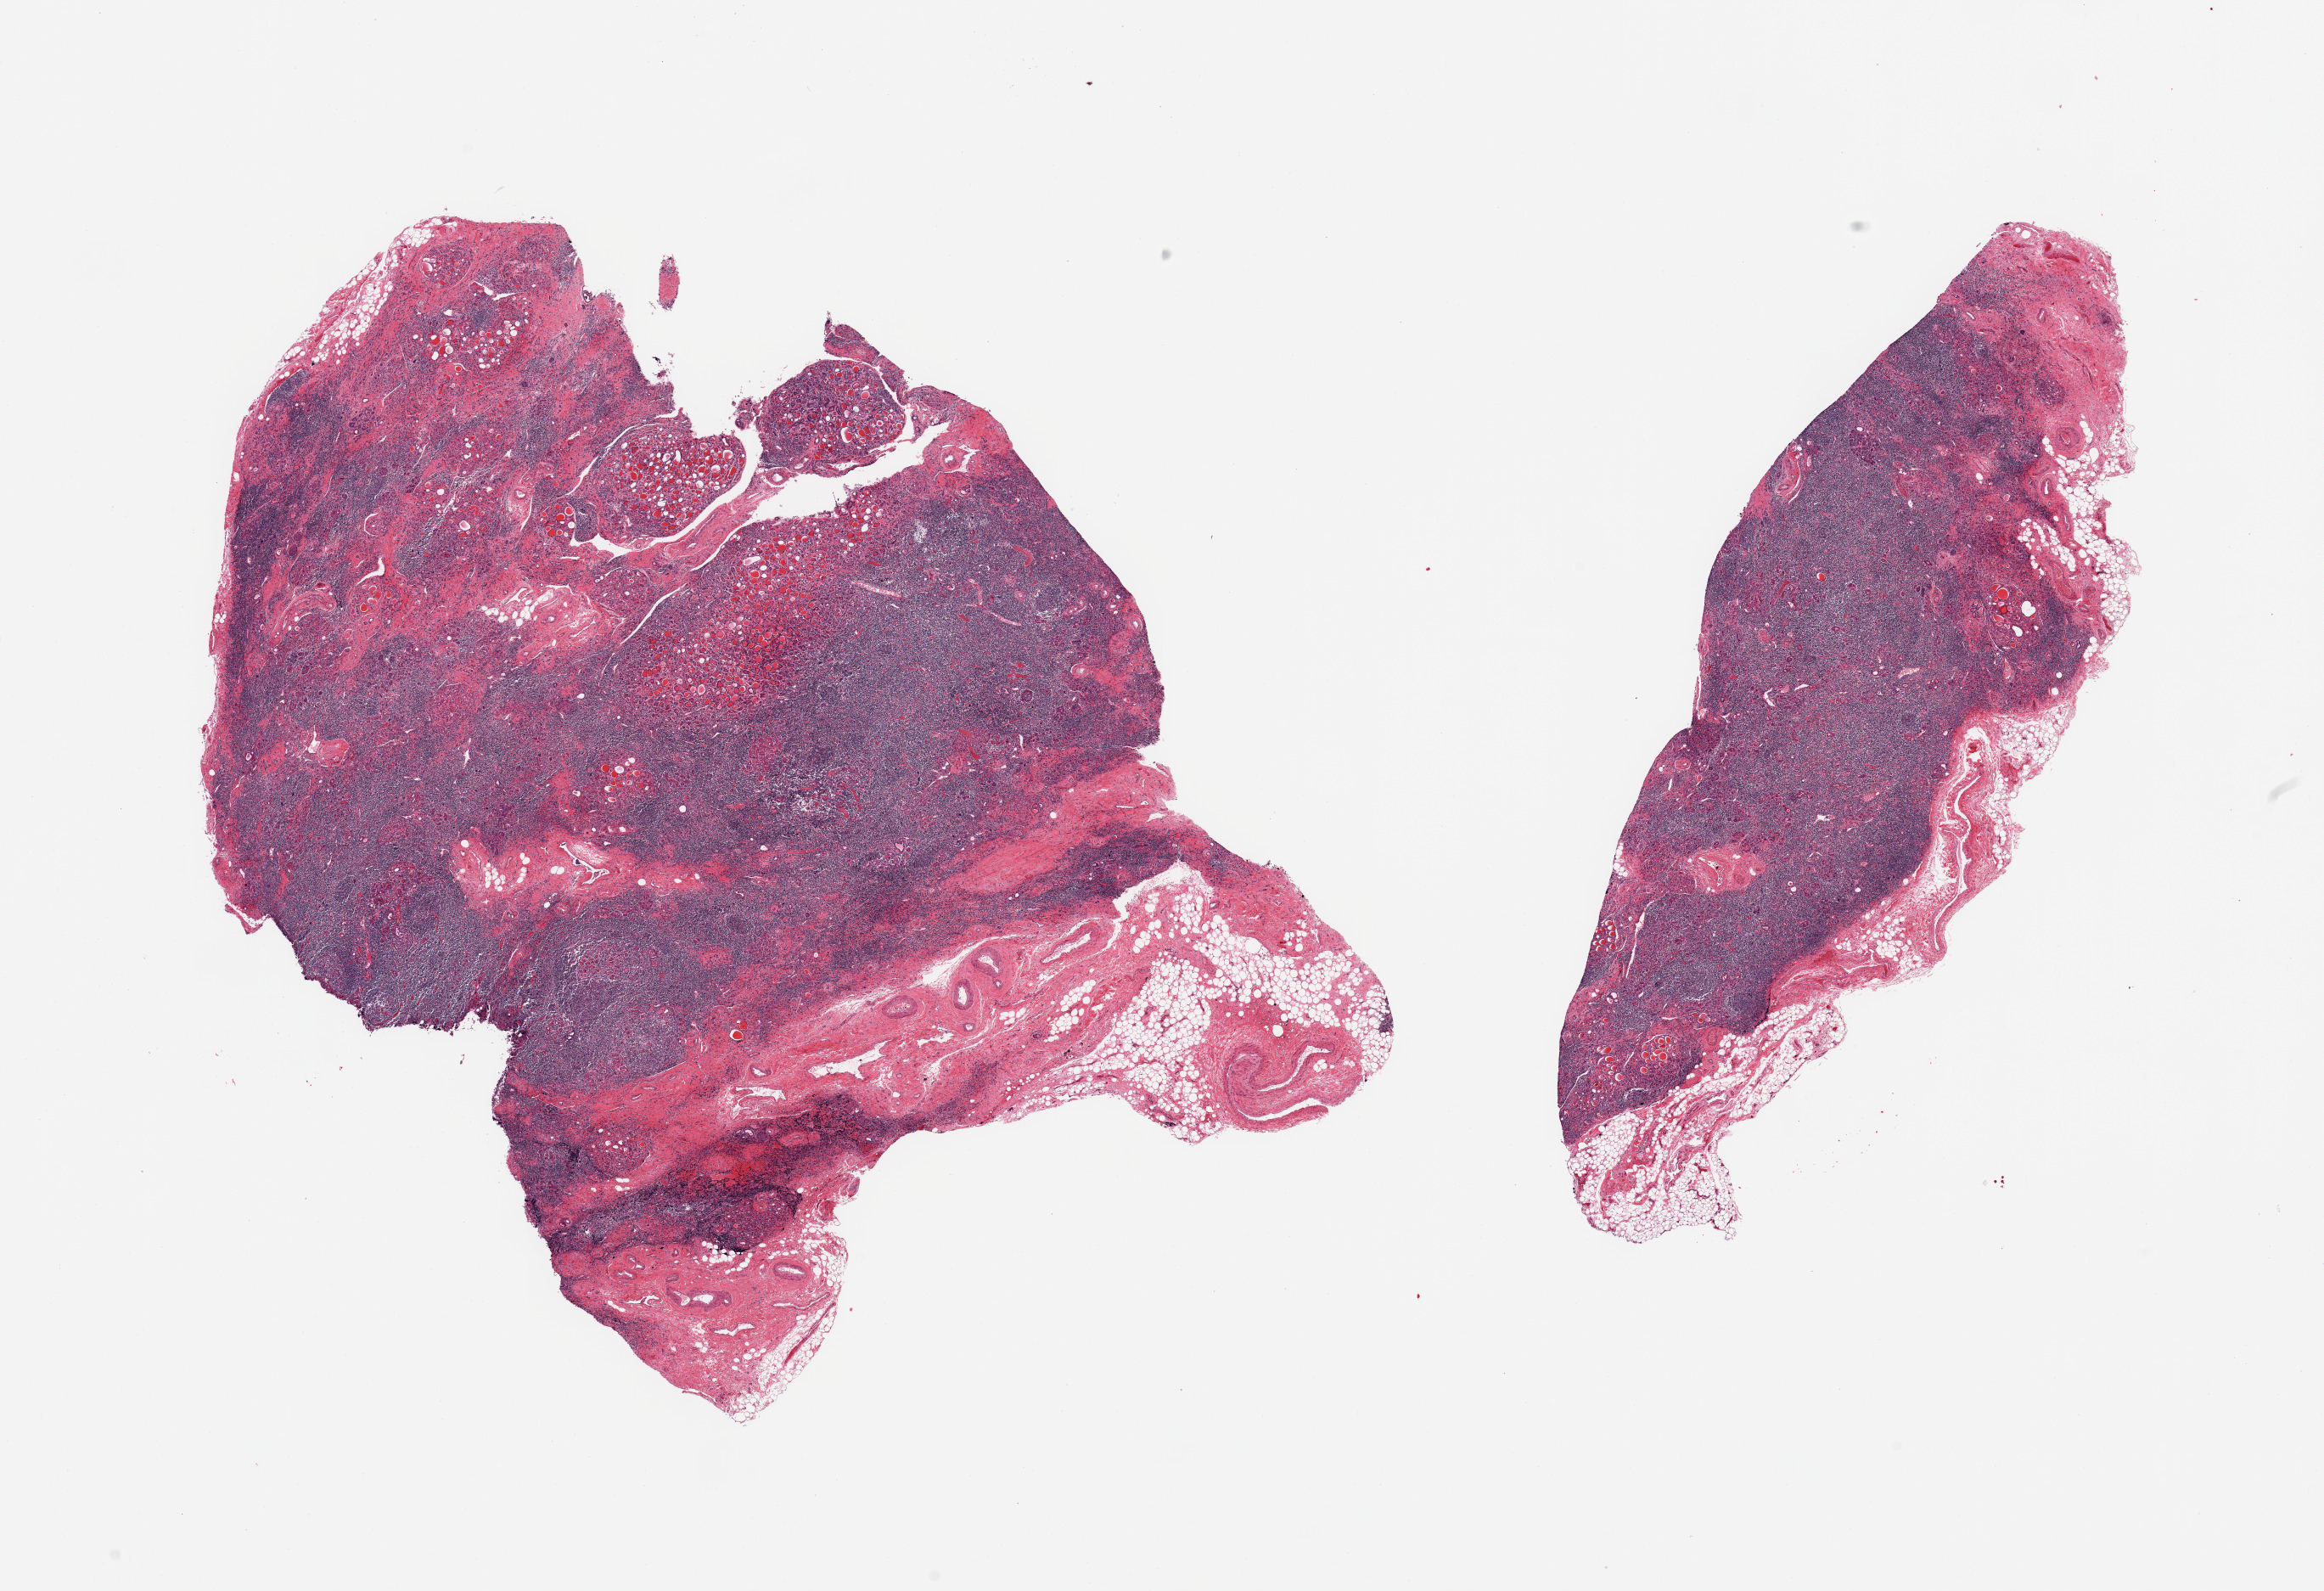
Hematoxylin and eosin (H&E) whole-slide image, brightfield — shown as a low-resolution overview of the whole scanned area (about 21.7 x 14.8 mm, acquisition: 20x scan), PAXgene-fixed, paraffin-embedded tissue, section of thyroid (target tissue), tissue donor sample. Donor sex: male.
• pathologist's review note for this sample: 2 pieces; lymphoplasmacytic infiltrate with reactive follicles, Hurthle cell change and metaplasia consistent with lymphocytic thyroiditis